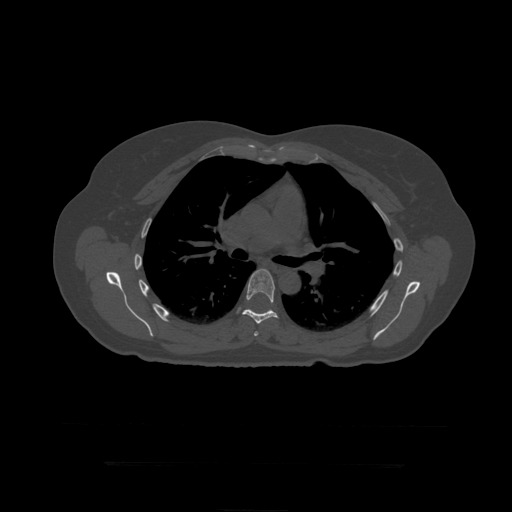
CT including the spine, one axial slice; position 302 of 399 along the scan axis; bone window (W 1800 / L 400 HU); 512 × 512 image matrix, field of view 450 × 450 mm. Patient age 41 years. Case-level facts recorded for this patient, not image findings: primary cancer: breast.
Annotated regions visible in this slice (semi-automatically segmented with operator editing):
- T6 vertebra: box from (x=254, y=331) to (x=259, y=336) px
- T7 vertebra: (x=242, y=269)–(x=279, y=324)